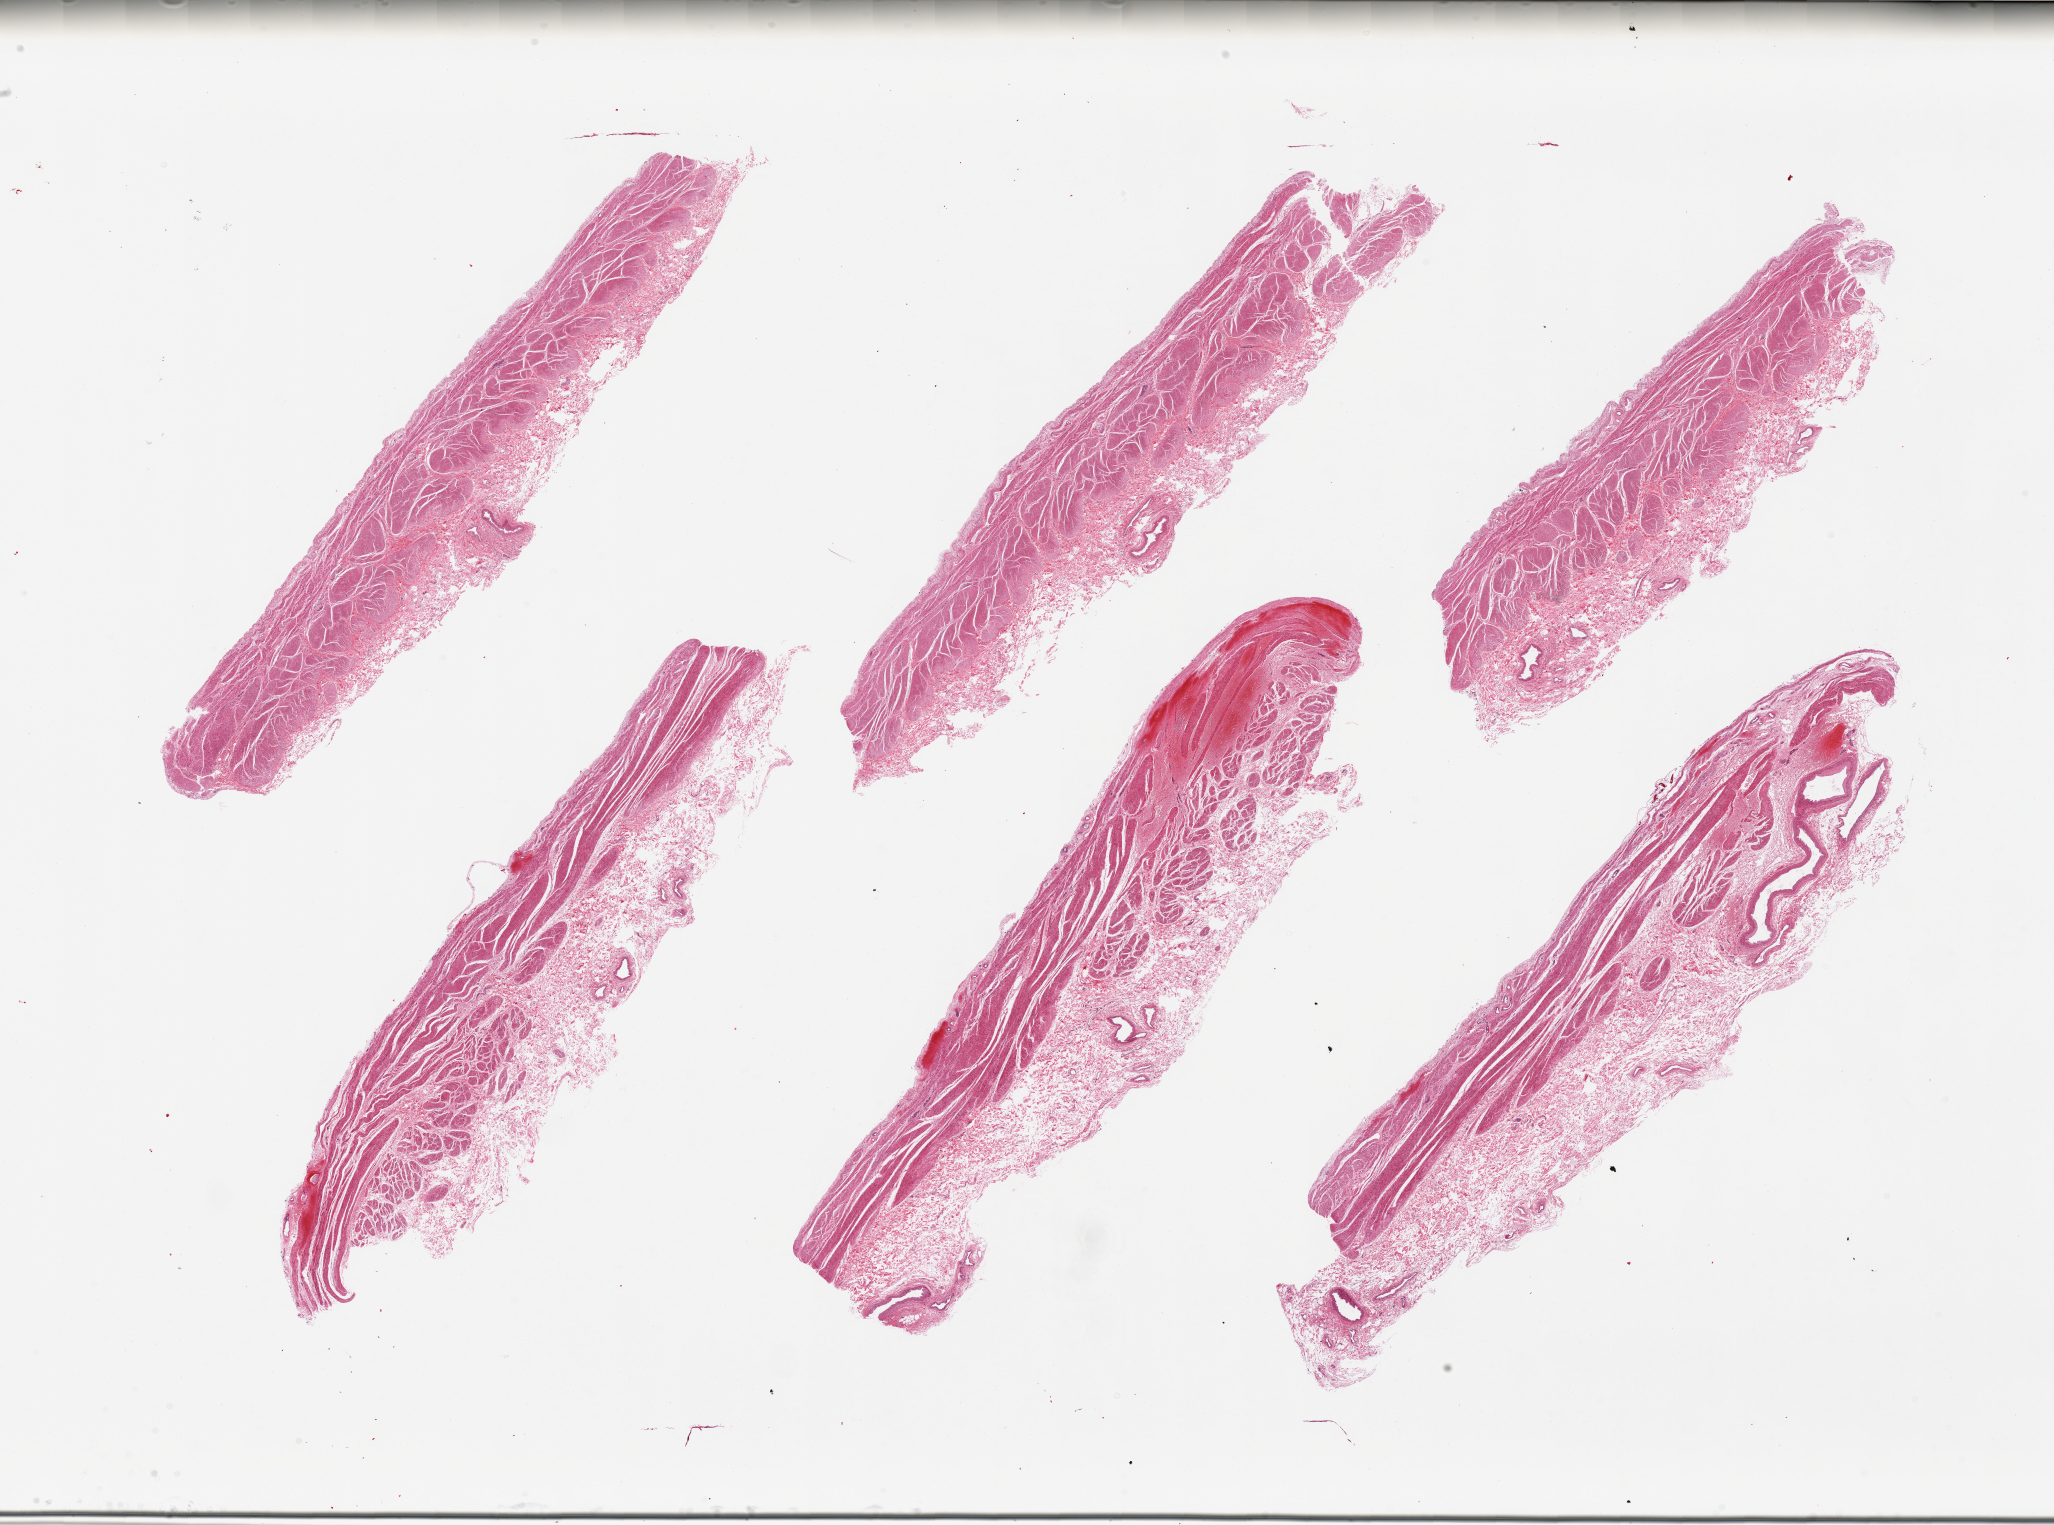
Digitized H&E-stained section, shown as a low-resolution overview of the whole scanned area (about 32.5 x 24.1 mm). PAXgene-fixed paraffin-embedded (PFPE) section. Section of stomach (target tissue). Donor tissue sample. Female donor.
• reviewer comment on this tissue sample: 6 pieces; mucosa absent on all 6 pieces, can only be used for muscularis propria assessment